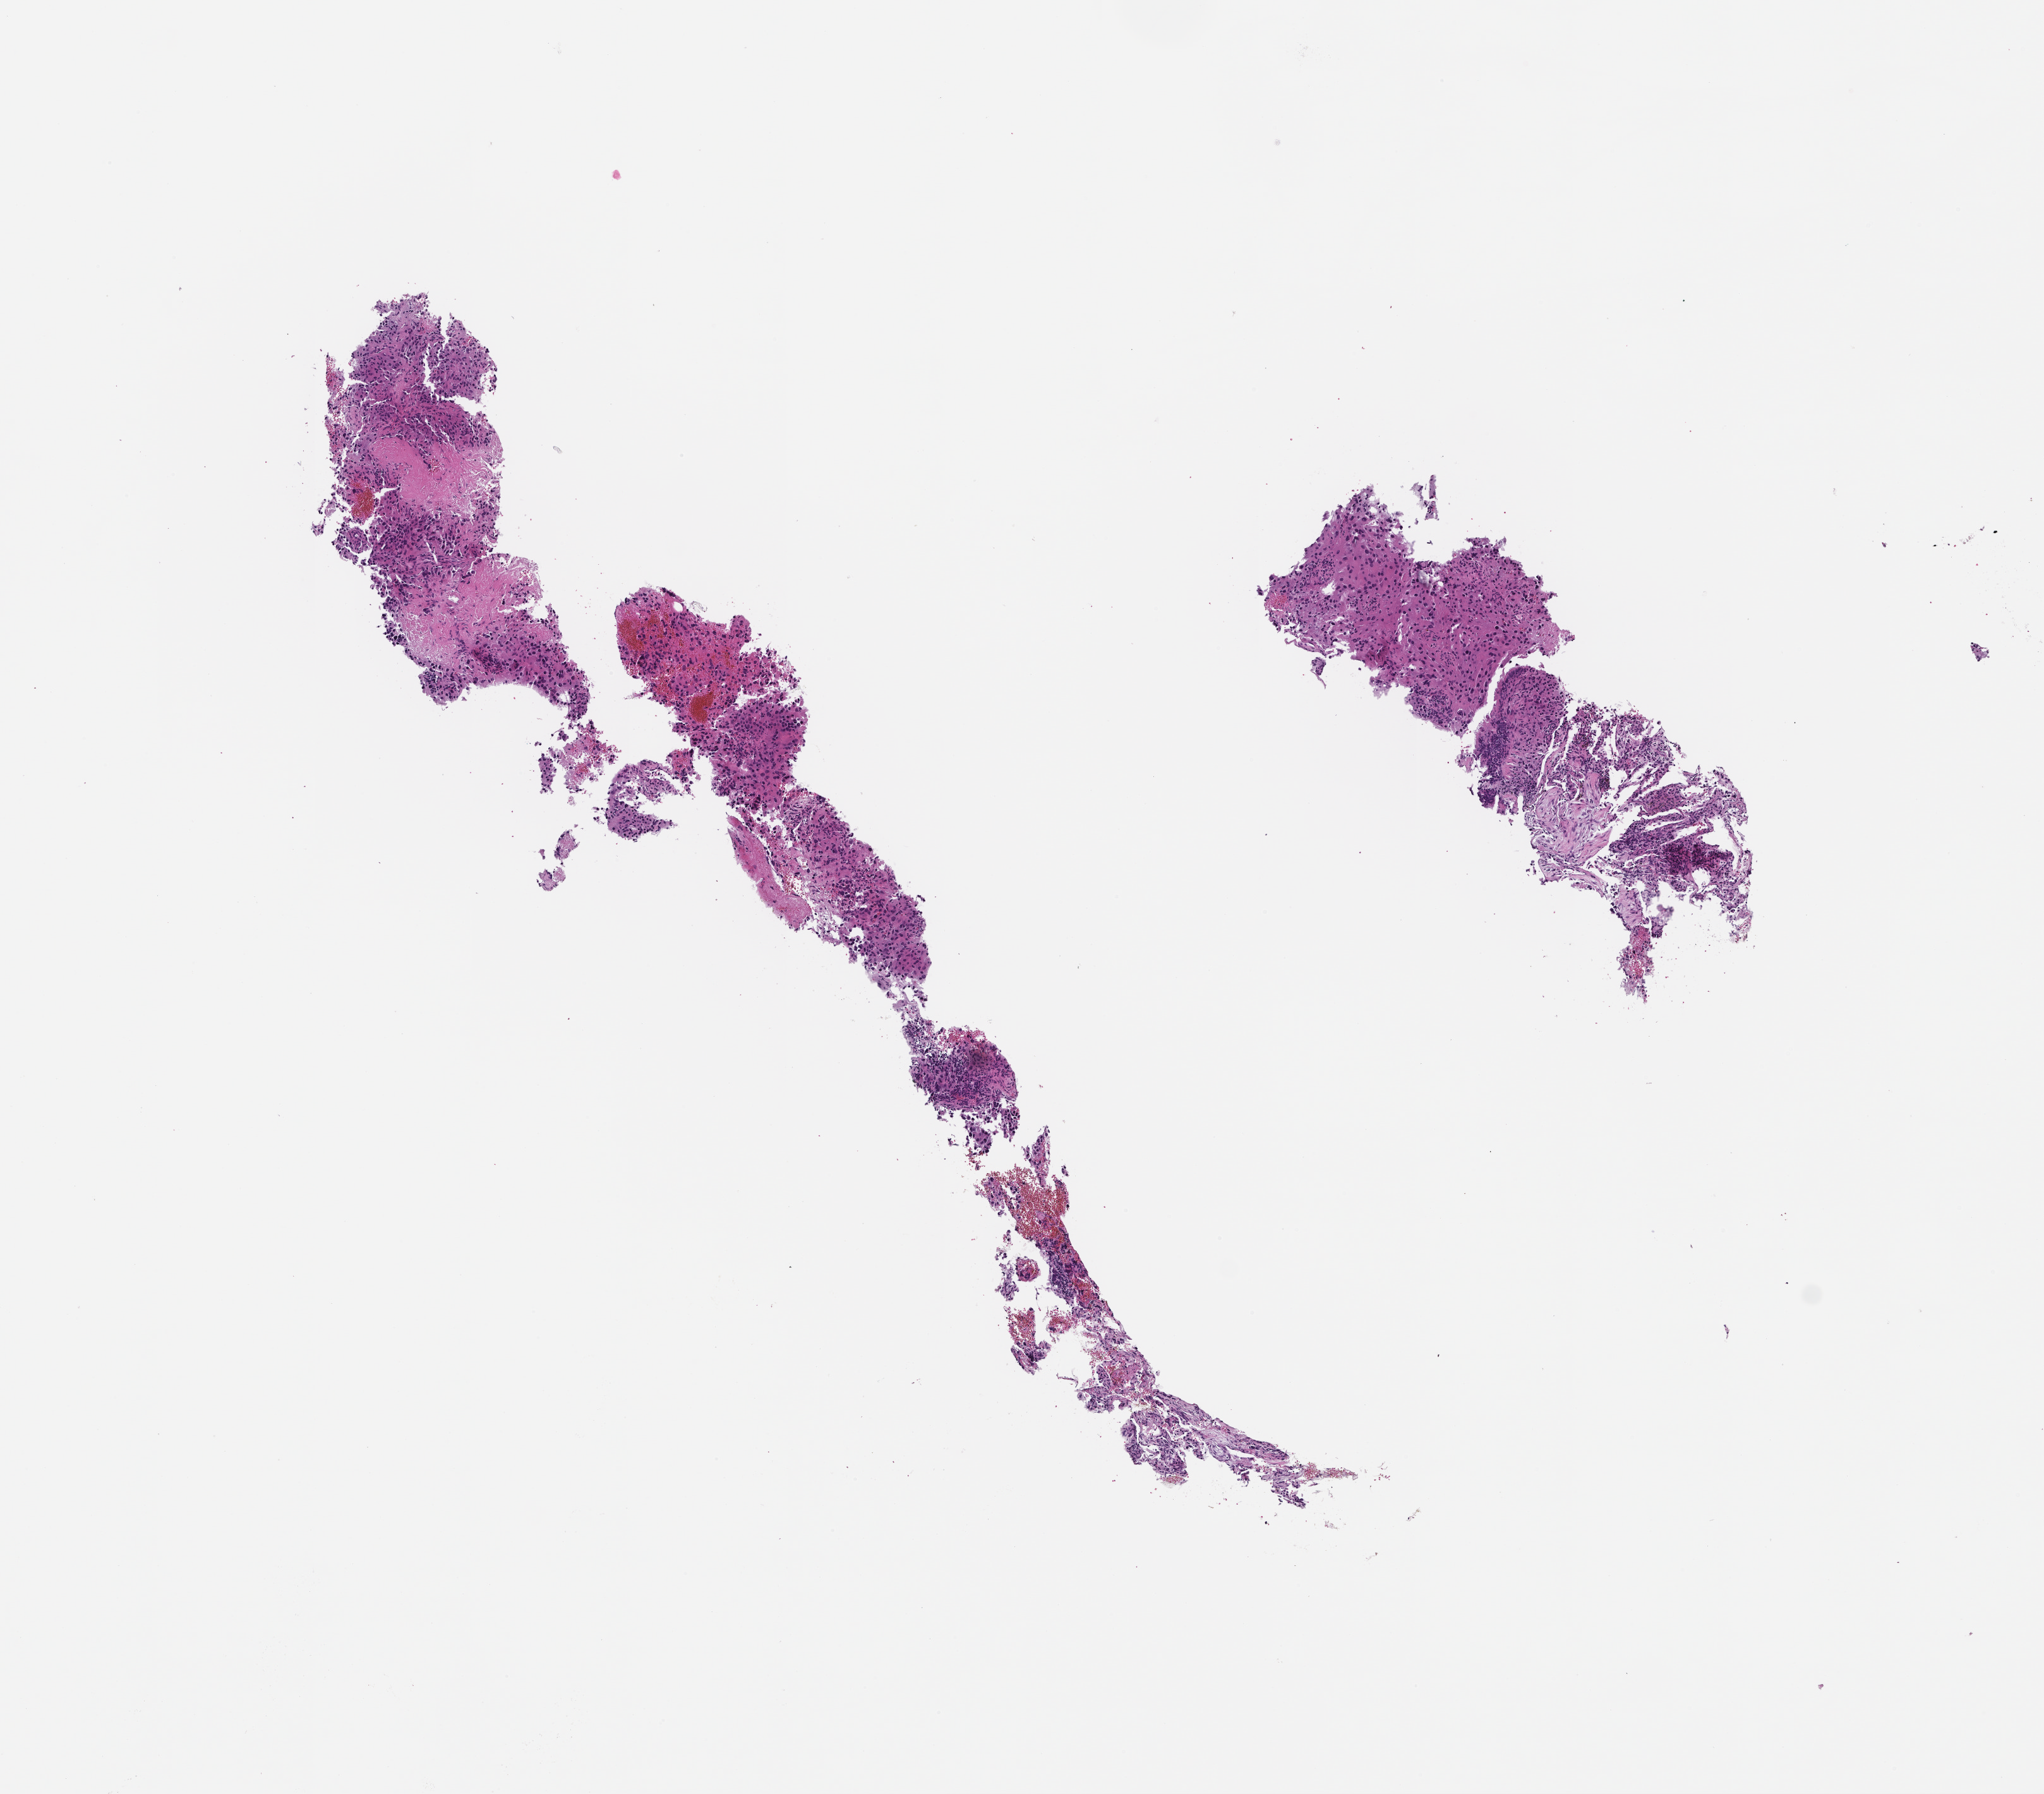
Hematoxylin and eosin (H&E) whole-slide image — shown as a low-resolution overview of the whole scanned area (about 6.5 x 5.7 mm), FFPE section, specimen time point: archival tissue. Patient: male.
• this section: metastatic tumor tissue
• primary diagnosis of the patient: Melanoma